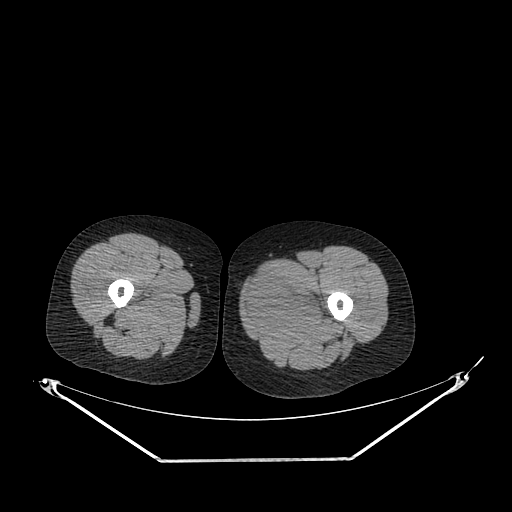
CT of an extremity soft-tissue mass (from a PET/CT study), one axial slice. Position 229 of 267 along the scan axis. Reconstruction kernel SOFT. 120 kVp. Soft-tissue window (W 400 / L 40 HU). 512 × 512 image matrix. Female patient. From the clinical record (not read from this slice): histological type: pleiomorphic leiomyosarcoma; grade: intermediate; site of the primary tumour: left thigh.
Structures marked on this image (expert contour drawn on MRI and transferred to this co-registered scan by the dataset authors):
- gross tumour volume including surrounding oedema: box from (x=244, y=272) to (x=330, y=328) px
- gross tumour volume (mass): (x=246, y=272)–(x=321, y=327)